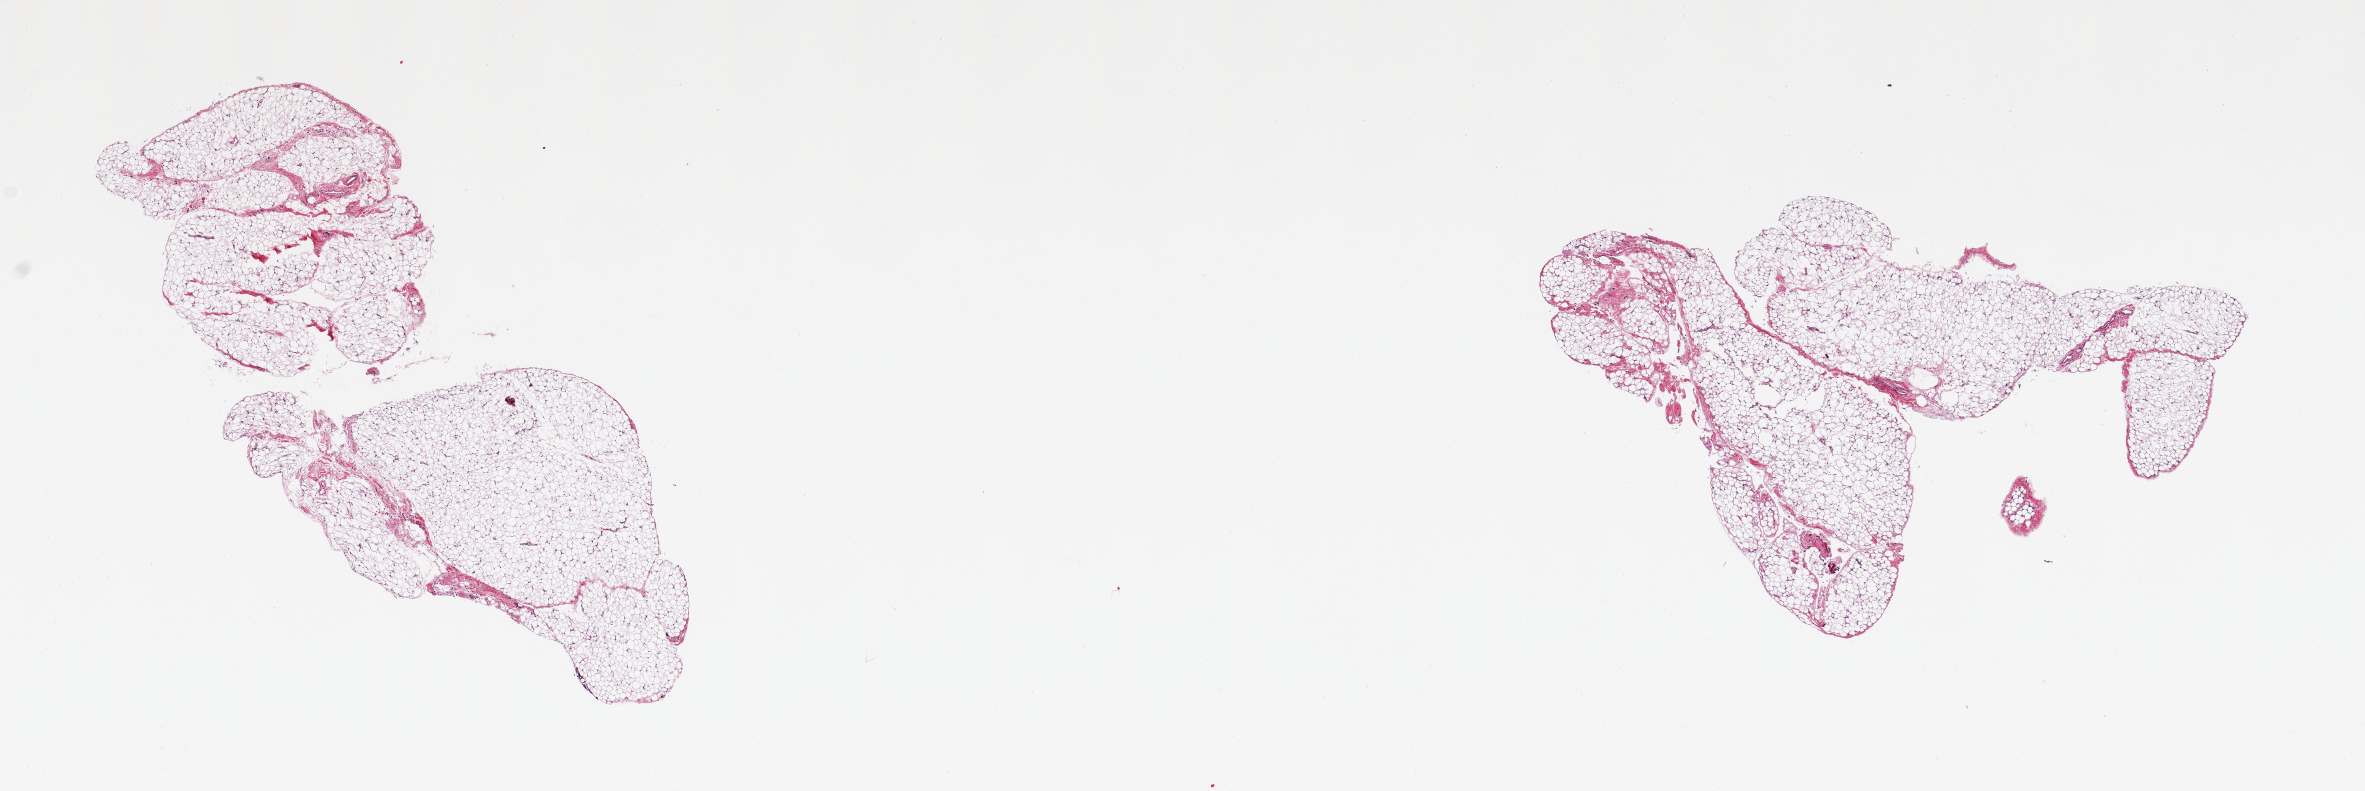
H&E whole-slide image — shown as a low-resolution overview of the whole scanned area (about 18.7 x 6.3 mm, from a 20x scan); PAXgene-fixed, paraffin-embedded tissue; sampled site (target tissue): omentum; tissue donor sample.
Reviewer comment on this tissue sample: 2 pieces; <5% fibrous content.